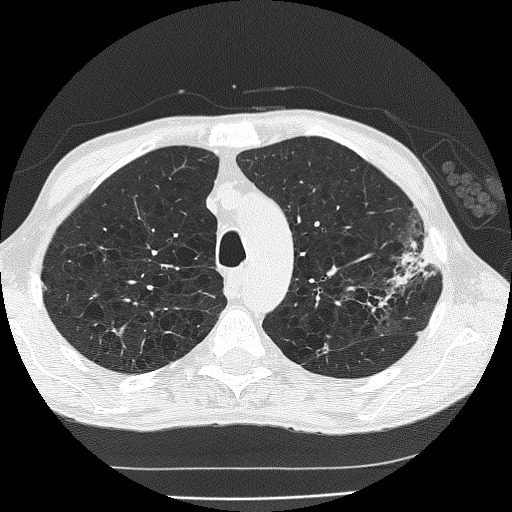
Low-dose screening chest CT, one axial slice; position 140 of 185 along the scan axis; 120 kVp; lung window (W 1500 / L -600 HU); 512 × 512 image matrix, field of view 320 × 320 mm.
Annotated regions visible in this slice (manually delineated by an expert):
- lesion 1 (tumor, upper lobe of left lung): box from (x=391, y=242) to (x=432, y=287) px